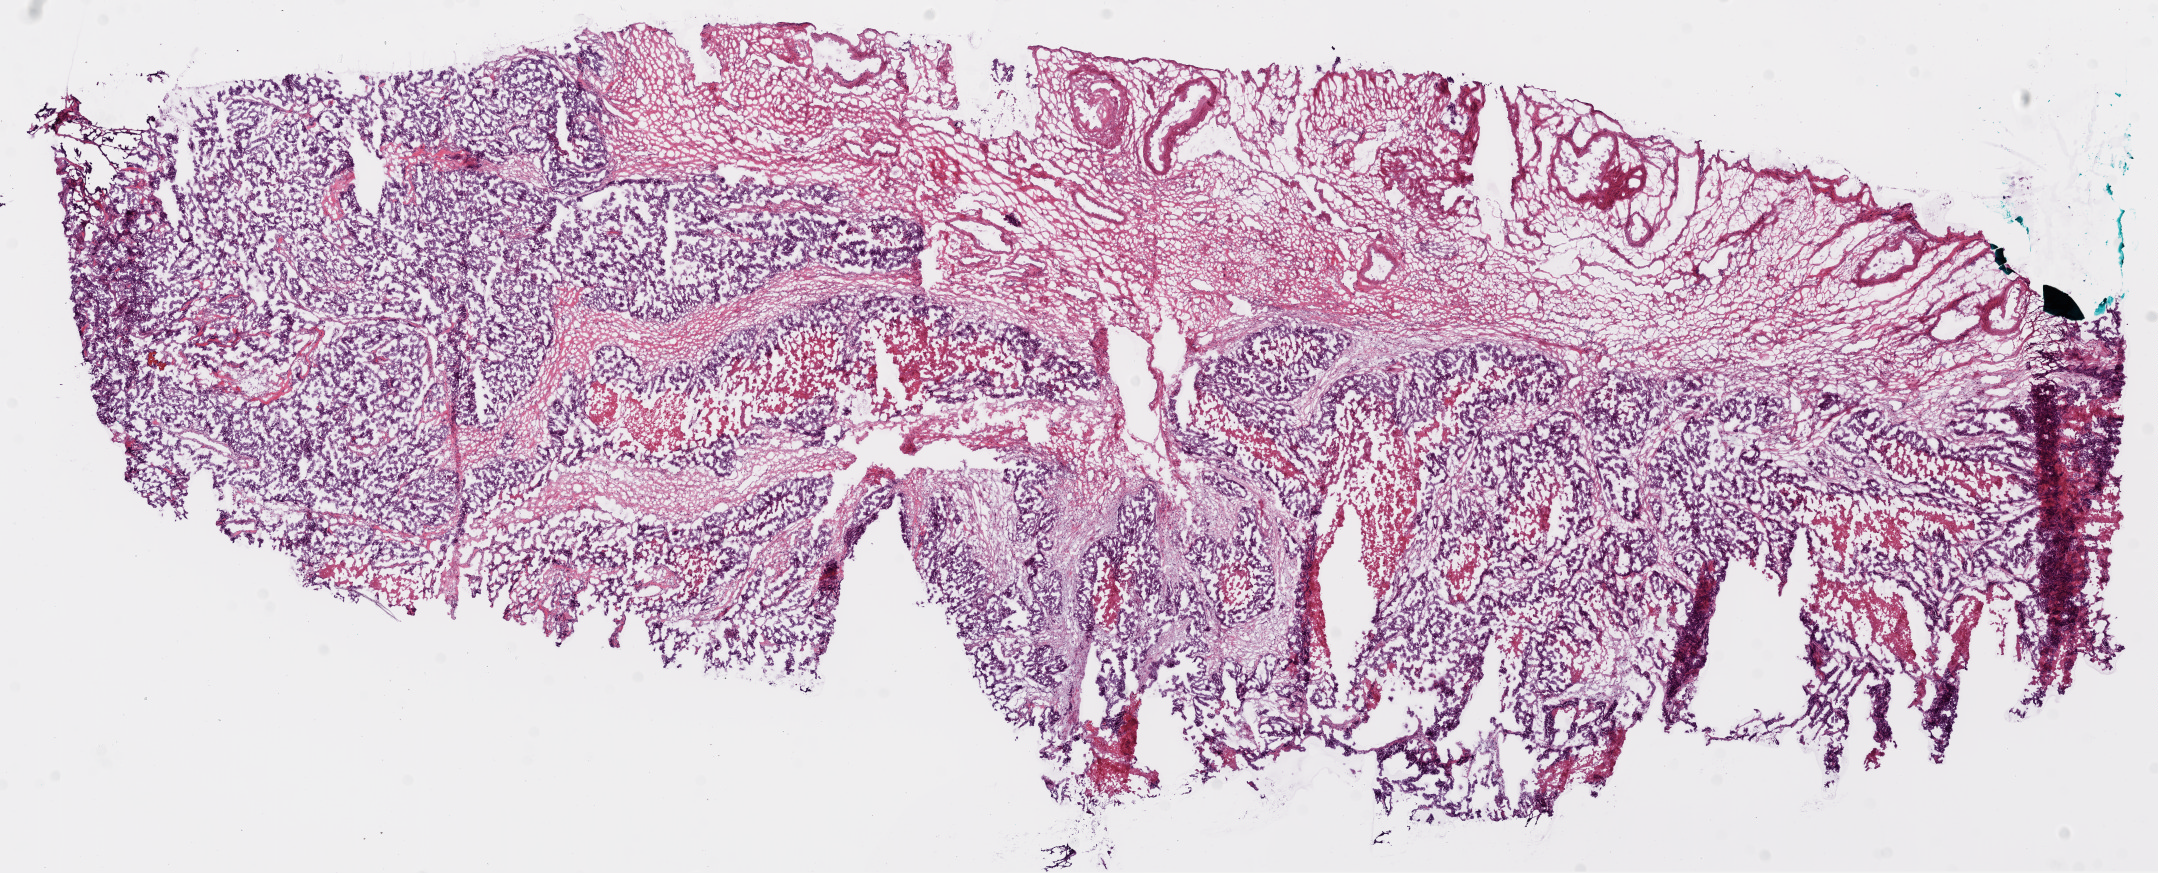
Whole-slide histology image, H&E-stained — a low-resolution overview of the entire scanned area, about 17.4 x 7.0 mm (acquisition: 20x scan). Frozen section. Primary tumour sample from the ovary. Patient: female, age at initial diagnosis 76 years. Histologic grade: G2 (moderately differentiated). Pathologist review of this section (percent, as recorded): tumour cells 40%, tumour nuclei 80%, normal cells 0%, stromal cells 40%, necrosis 20%.
• FIGO stage: IIIC
• histologic diagnosis: Serous cystadenocarcinoma, NOS